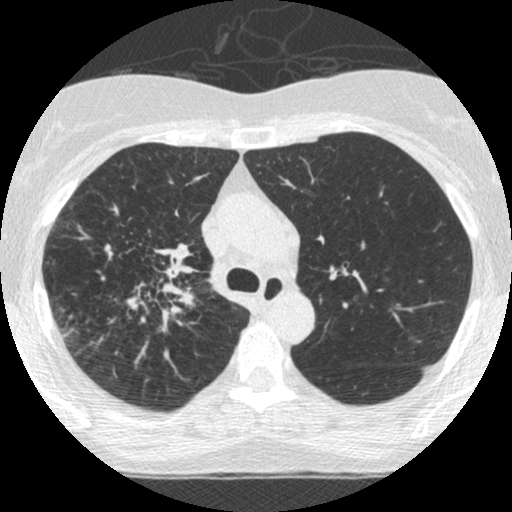
Low-dose screening chest CT, one axial slice; slice 182 of 253 in the series (ordered by position); reconstruction kernel STANDARD; 120 kVp; lung window (W 1500 / L -600 HU); 1.25 mm slice thickness; 512 × 512 image matrix, field of view 294 × 294 mm.
Structures marked on this image (outlined manually by an expert reader):
- lesion 2 (tumor, hilum of right lung): box from (x=129, y=242) to (x=199, y=335) px